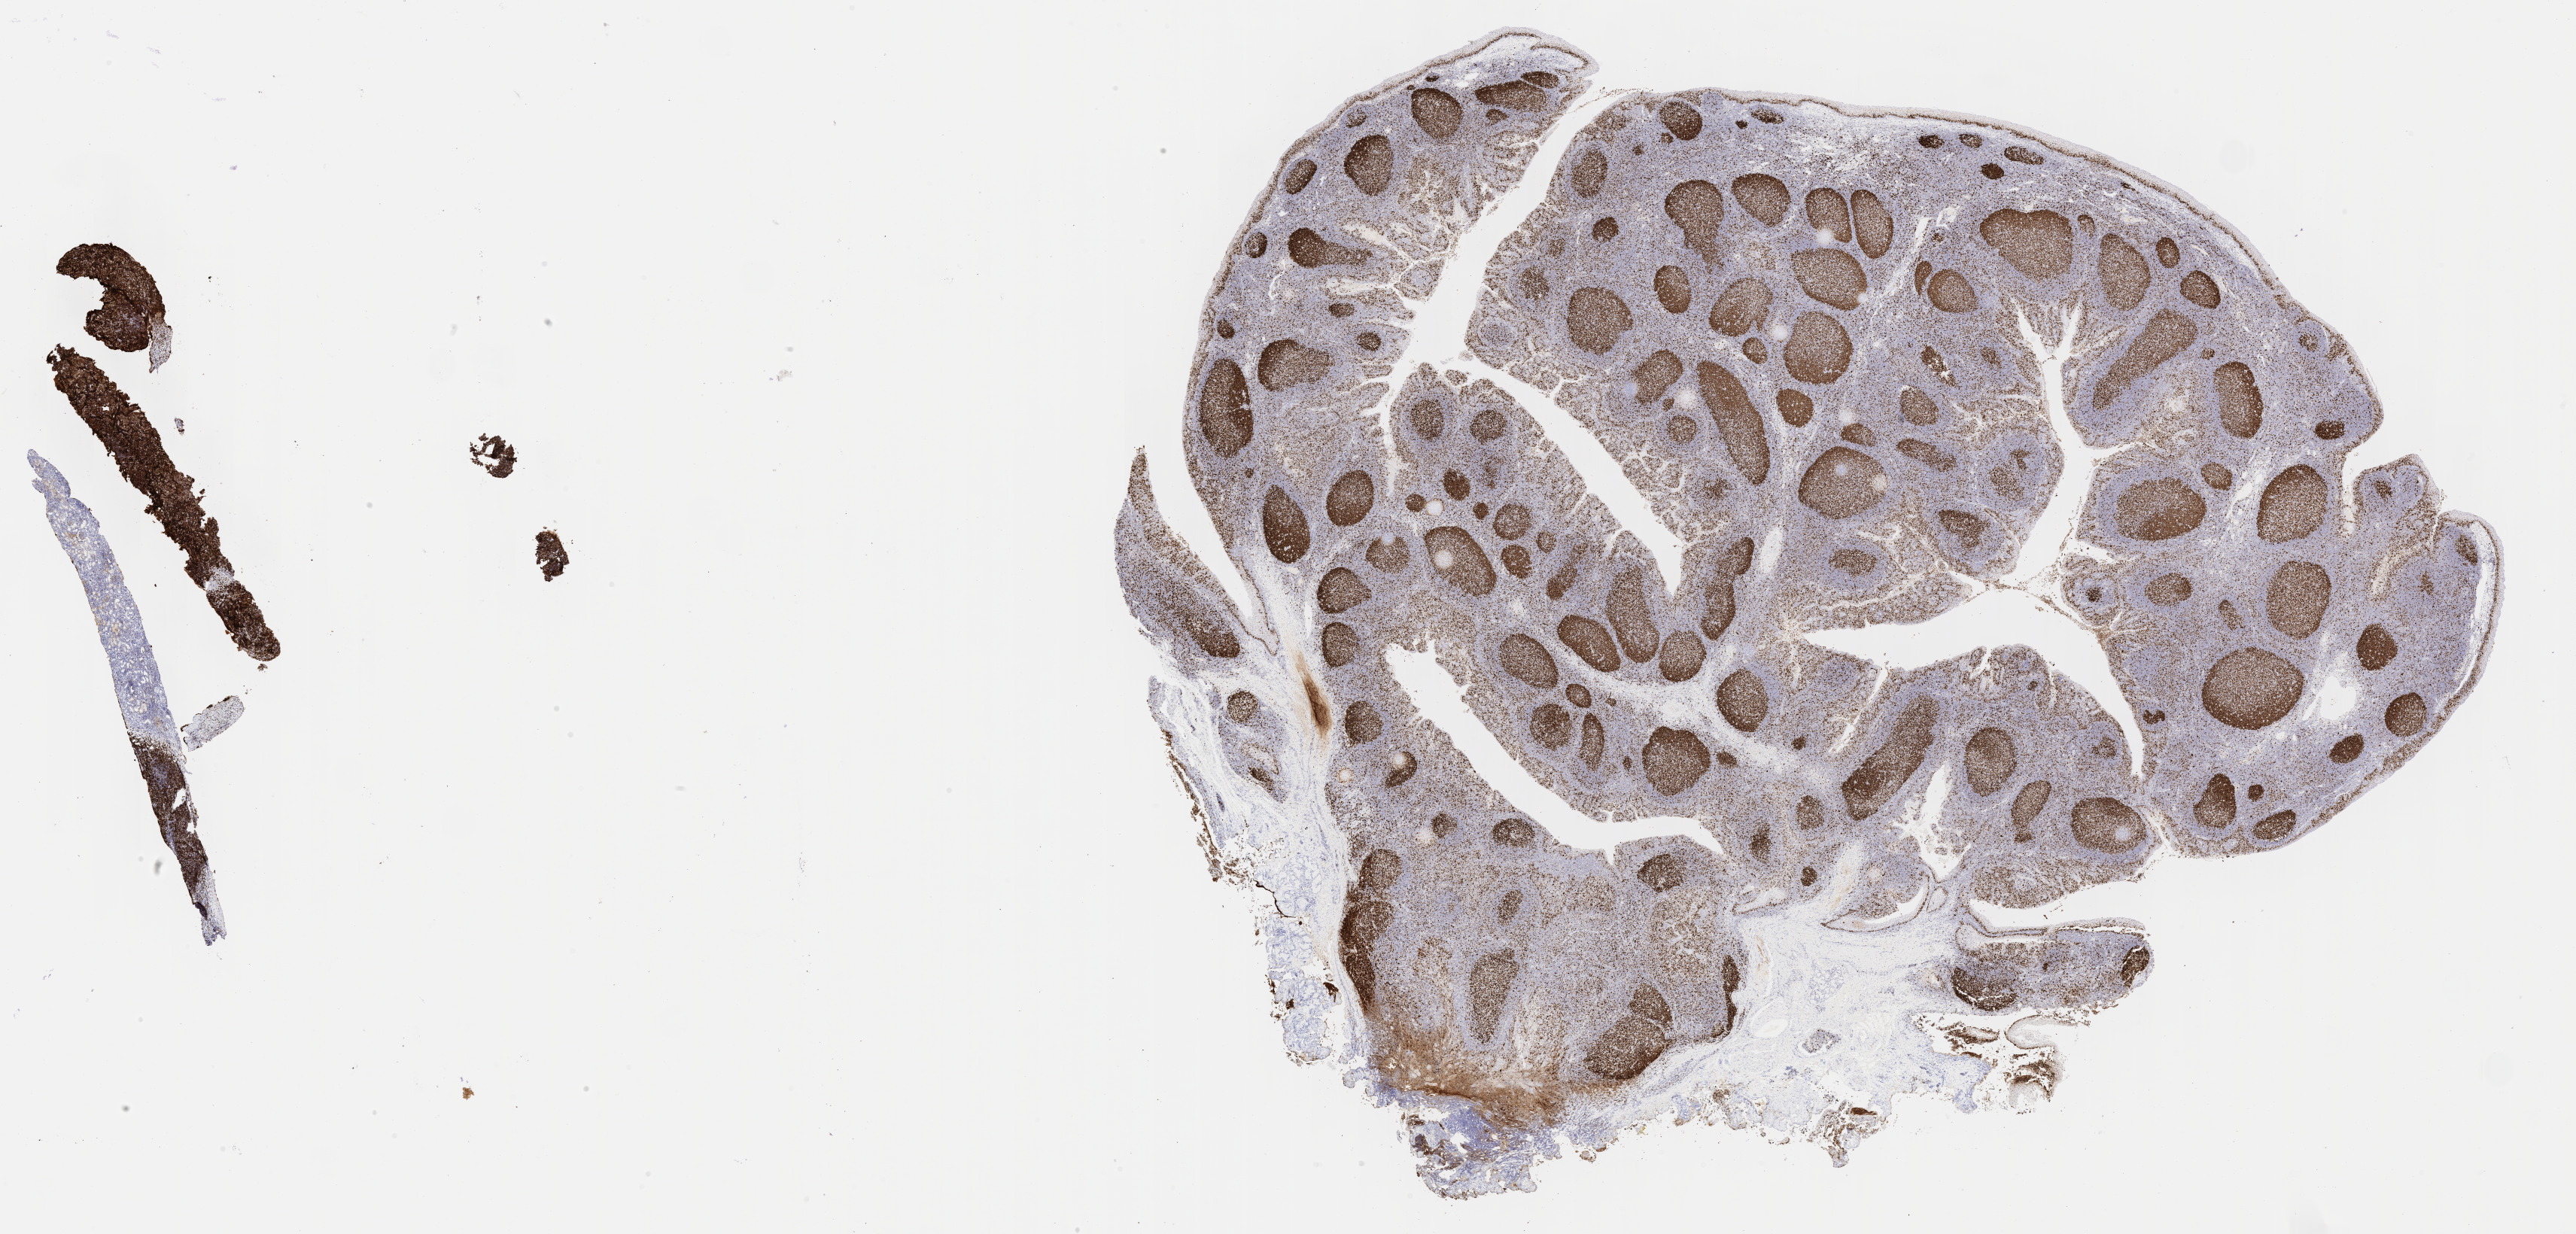
Immunohistochemistry (IHC) whole-slide image stained for Ki-67, low-resolution overview of the scanned area, about 27.7 x 13.3 mm, specimen: tumor tissue, site: liver. Male patient; age at initial diagnosis 8 years.
• diagnosis: Burkitt lymphoma, NOS